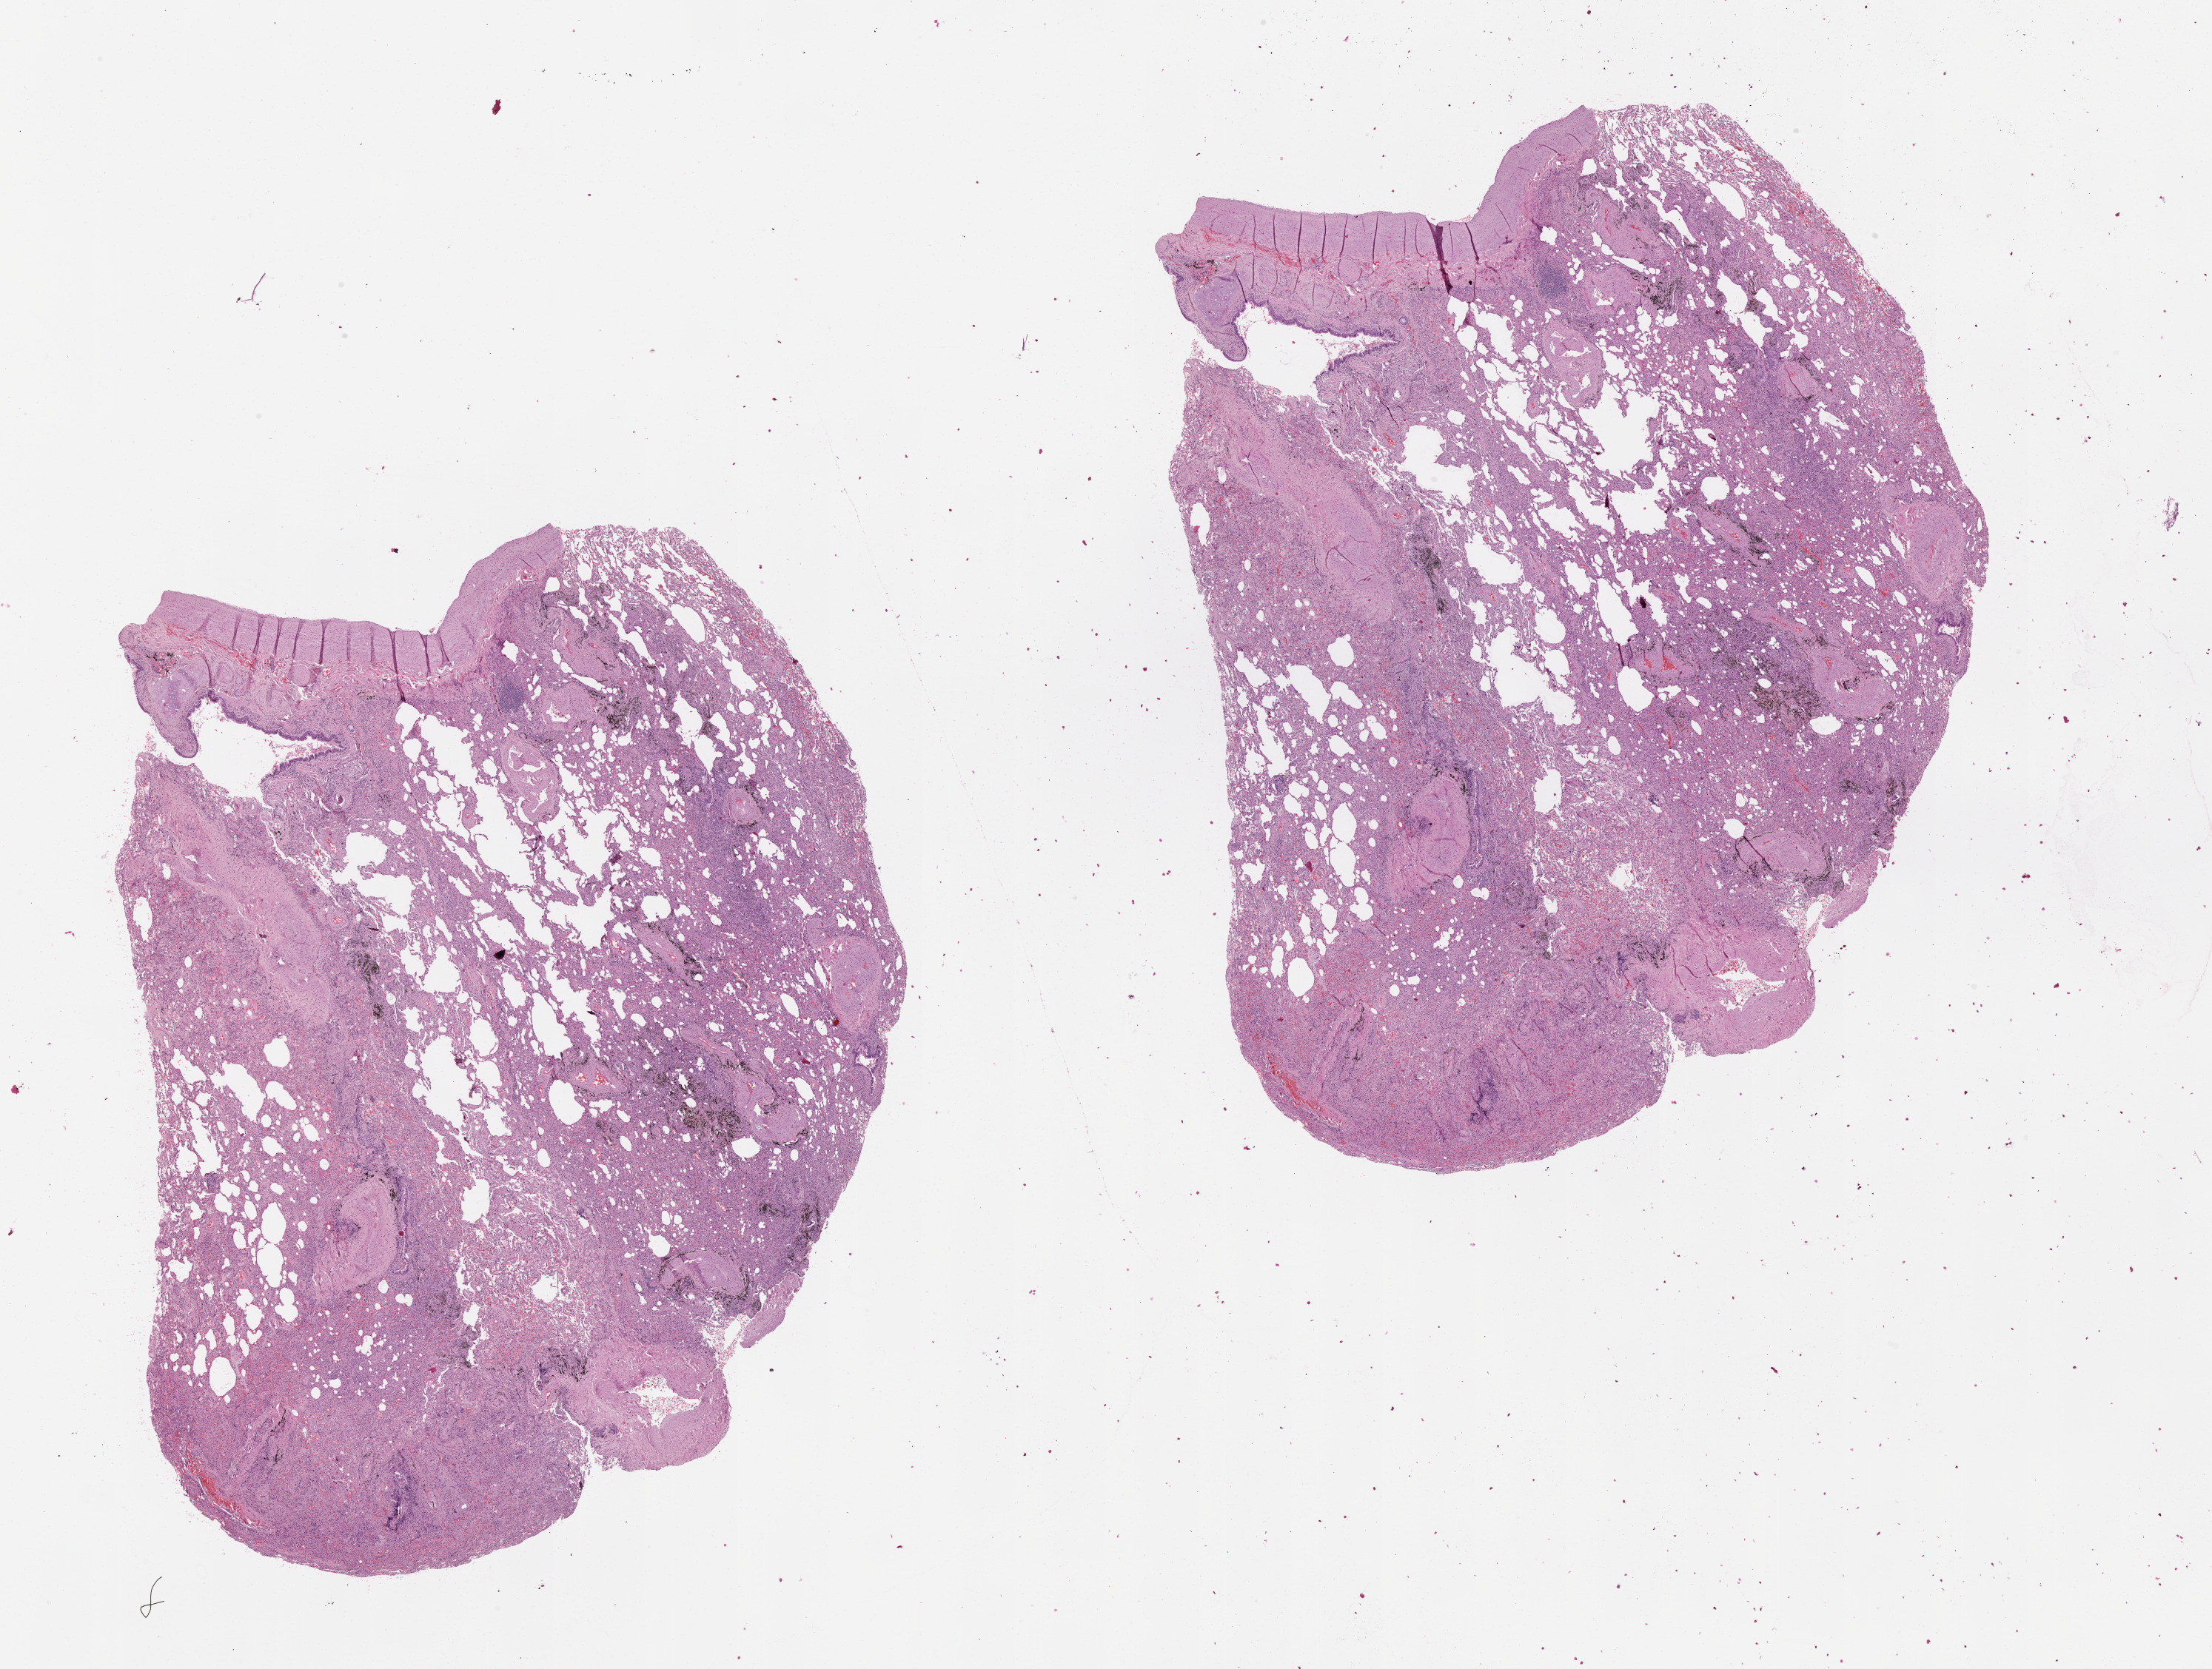
Digitized Hematoxylin and eosin (H&E) stained tissue section (whole slide) — a low-resolution overview of the entire scanned area, about 24.1 x 18.2 mm. Normal (non-tumour) tissue sample, lung. Patient: male, age 69 years.
- this section: normal (non-tumour) tissue from the same patient
- patient diagnosis (cohort enrolment): squamous cell carcinoma (lung)